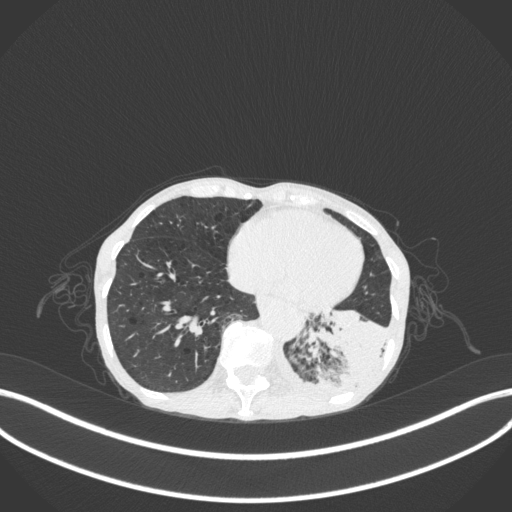
Chest CT, one axial slice. Slice 63 of 347 in the series (ordered by position). Reconstruction kernel B31f. 120 kVp. Lung window (W 1500 / L -600 HU). 1 mm slice thickness. 512 × 512 image matrix. Patient: female, 70 years. Case-level facts recorded for this patient, not image findings: clinical TNM (as recorded): T3 N0 M0.
Outlined on this slice (bounding box drawn by a radiologist):
- lung tumour (recorded histology: small cell carcinoma): bounding box <303,300,395,407> (left, top, right, bottom; pixels)